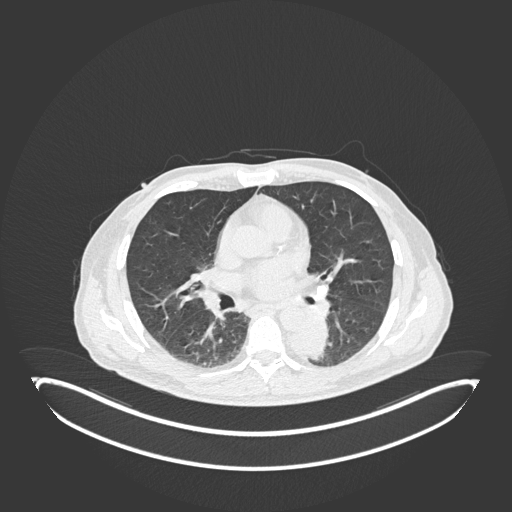
Chest CT, one axial slice; position 103 of 251 along the scan axis; 120 kVp; lung window (W 1500 / L -600 HU); 512 × 512 image matrix. Patient: male, 72 years. From the clinical record (not read from this slice): clinical TNM (as recorded): T2b N0 M1.
Outlined on this slice (bounding box drawn by a radiologist):
- lung tumour (recorded histology: adenocarcinoma): bounding box (x1, y1, x2, y2) in pixels: (287, 306, 332, 363)